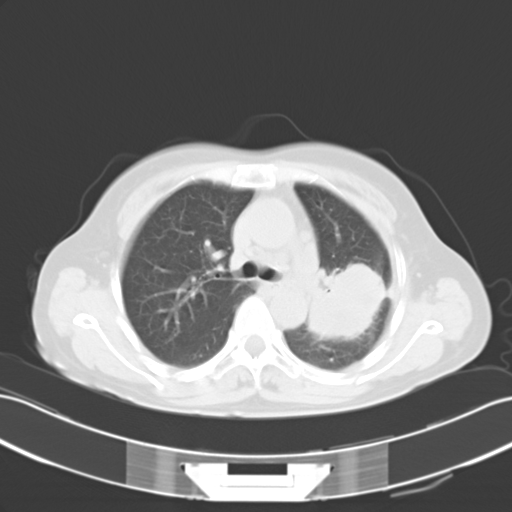
Chest CT, one axial slice. Position 17 of 25 along the scan axis. Reconstruction kernel B40f. 120 kVp. Lung window (W 1500 / L -600 HU). 10 mm slice thickness. 512 × 512 image matrix, field of view 353 × 353 mm. Female patient, age 54 years. Case-level facts recorded for this patient, not image findings: clinical TNM (as recorded): T3 N1 M0.
Outlined on this slice (rectangle marked by the reading radiologist):
- lung tumour (recorded histology: adenocarcinoma): bounding box (x1, y1, x2, y2) in pixels: (313, 250, 379, 346)